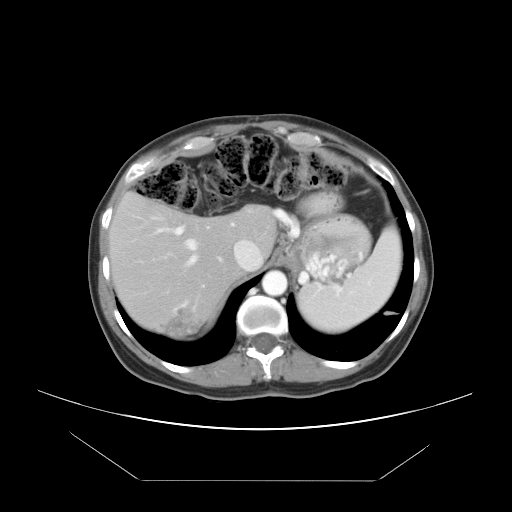
Contrast-enhanced abdominal CT, one axial slice; slice 34 of 45 in the series (ordered by position); reconstruction kernel STANDARD; 120 kVp; intravenous contrast given; soft-tissue window (W 400 / L 40 HU); 512 × 512 image matrix. Female patient, age 52 years. From the clinical record (not read from this slice): diagnosis: colorectal cancer liver metastases, imaged before liver resection; multiple liver metastases: yes; largest metastasis: 2.5 cm; disease in both lobes: no.
Annotated regions visible in this slice (expert manual segmentation):
- hepatic veins: bounding box [x1, y1, x2, y2] px = [150, 214, 205, 288]
- liver: [112, 196, 276, 336]
- planned liver remnant (the part of the liver to remain after resection): [112, 196, 276, 313]
- portal vein (with intrahepatic branches): [156, 224, 233, 260]
- liver metastasis: [168, 308, 199, 335]